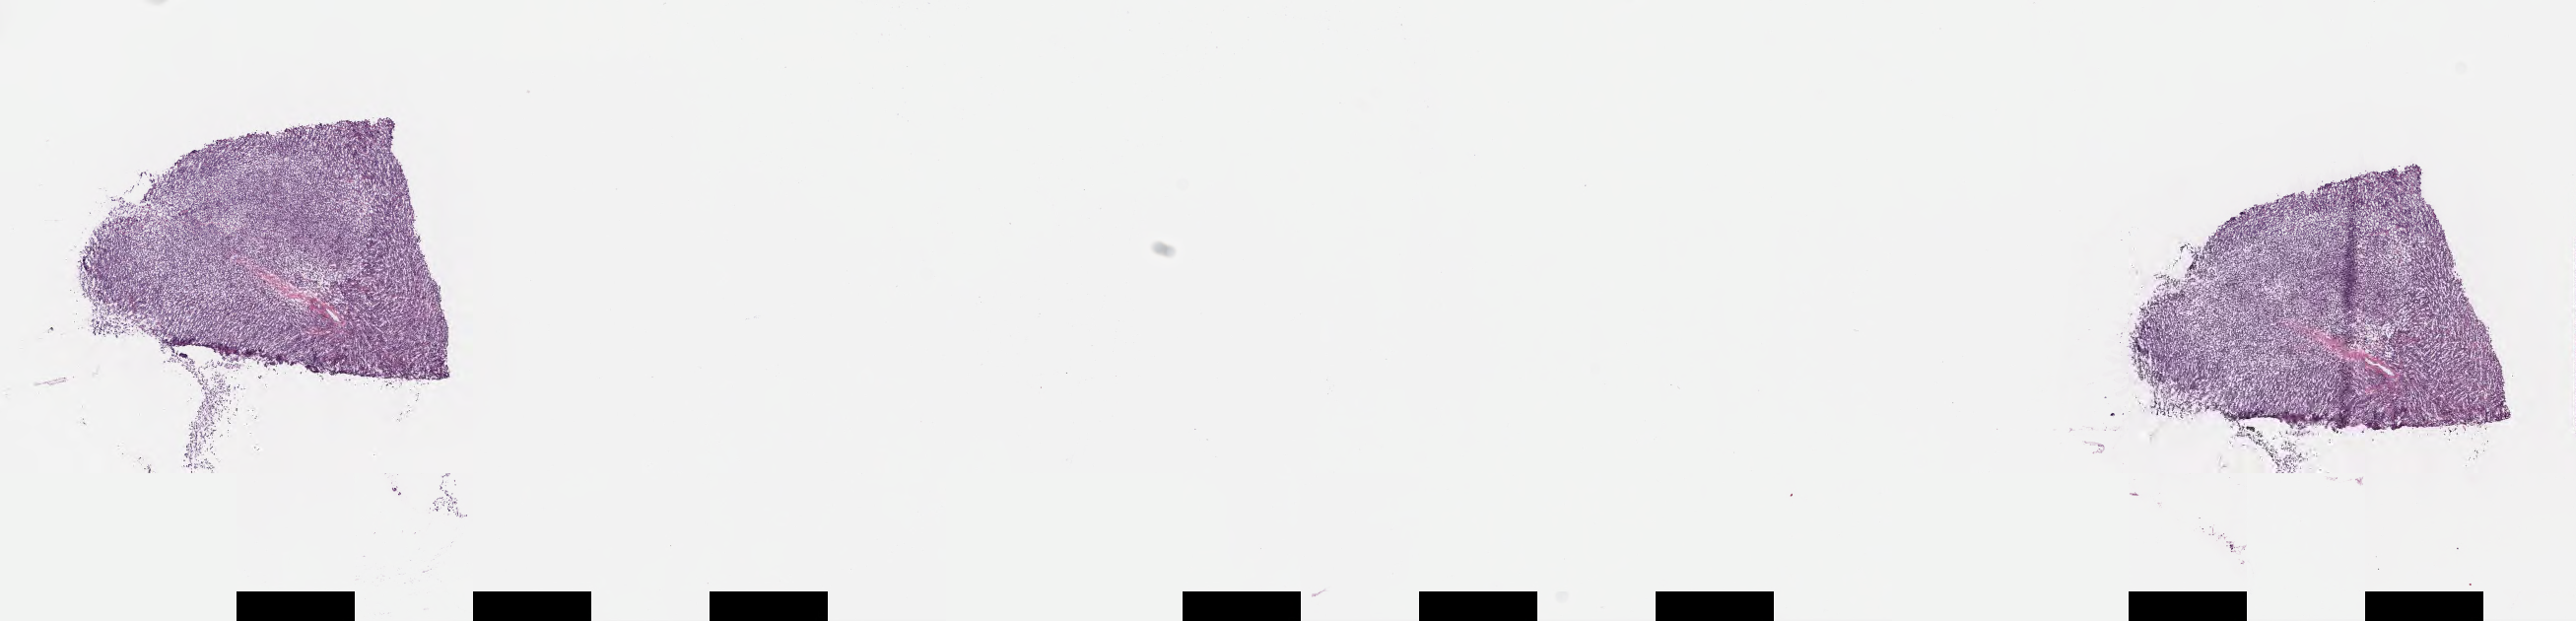
Hematoxylin and eosin (H&E) whole-slide image, low-resolution overview of the scanned area, about 21.1 x 5.1 mm; frozen section; specimen: primary tumor; site: buccal mucosa. Female, age 7 years at initial diagnosis. Composition of this section per pathologist review: tumor cells 90%, tumor nuclei 90%, stromal cells 10%, necrosis 0%, normal cells 0%. Inflammatory infiltration, as recorded: lymphocyte infiltration 80%, monocyte infiltration 10%, neutrophil infiltration 0%.
- Ann Arbor stage (patient): Stage III
- histologic diagnosis: Burkitt lymphoma, NOS